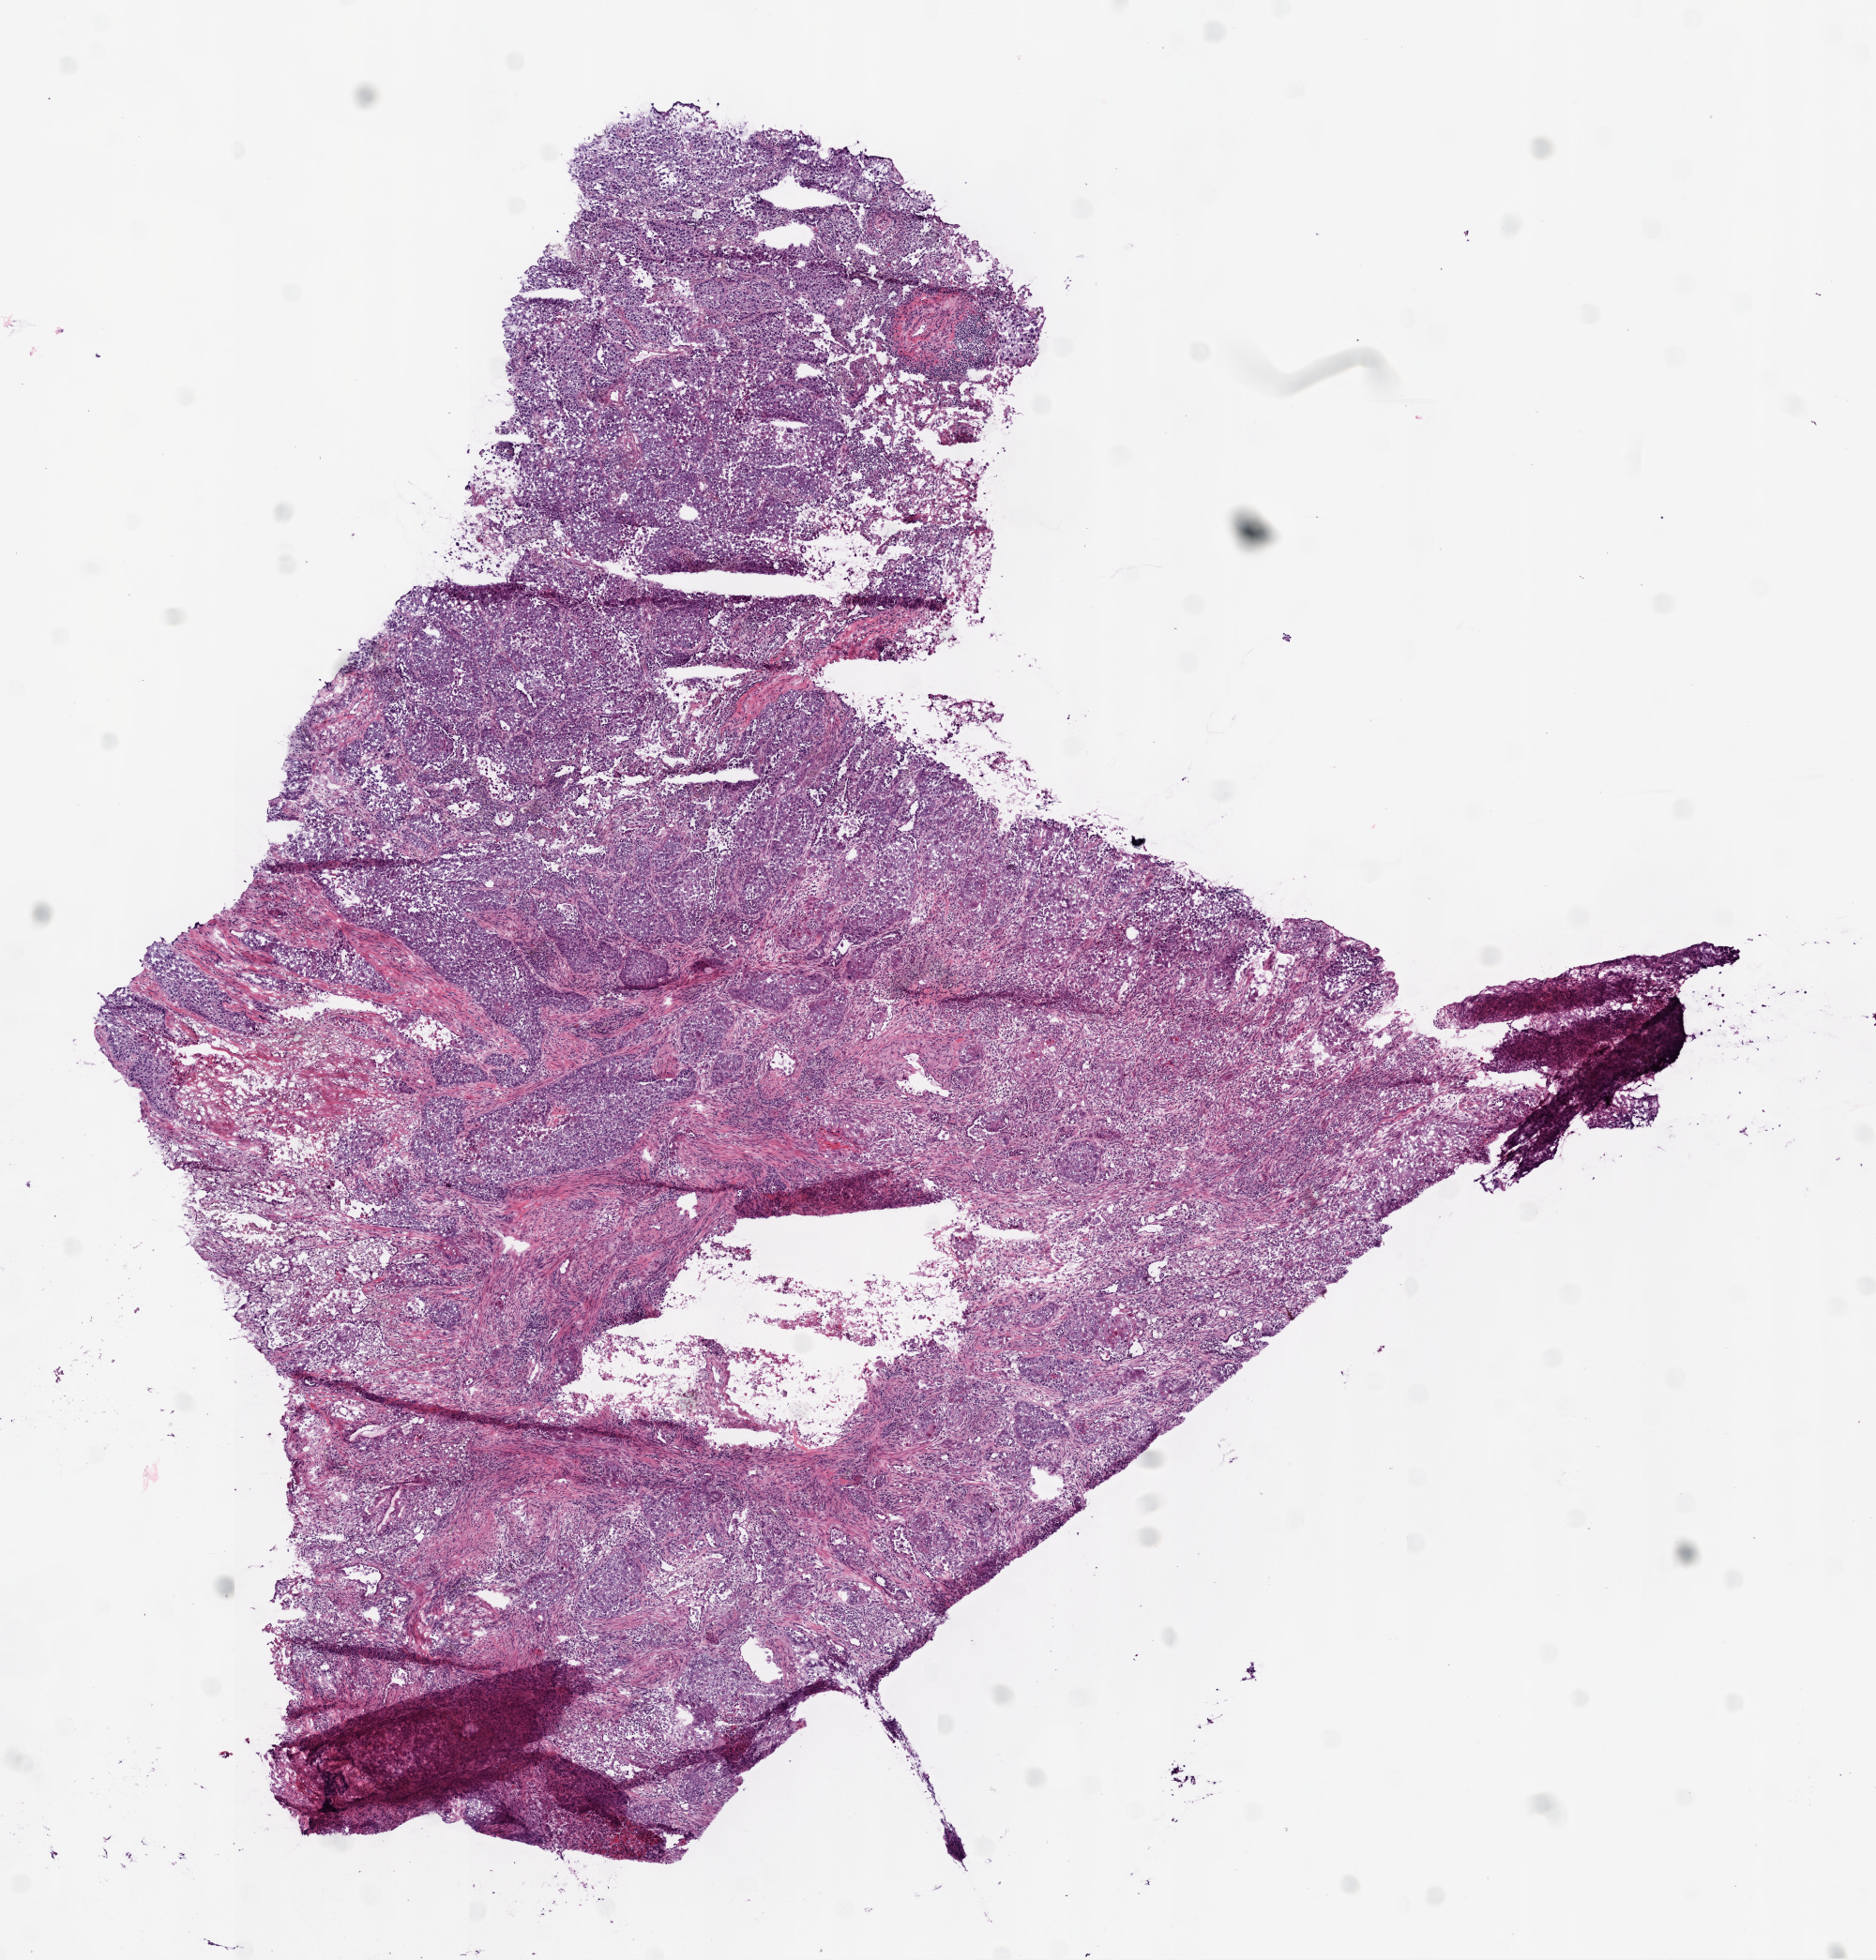
H&E whole-slide image, whole scanned area (about 8.0 x 8.4 mm, from a 20x scan) shown as a low-resolution overview; frozen section from the bottom of the tissue portion; sample: primary tumour, lung. Patient: male, age at initial diagnosis 71 years. Composition of this section per pathologist review: tumour cells 75%, tumour nuclei 75%.
Pathologic diagnosis: Squamous cell carcinoma, NOS (middle lobe, lung).